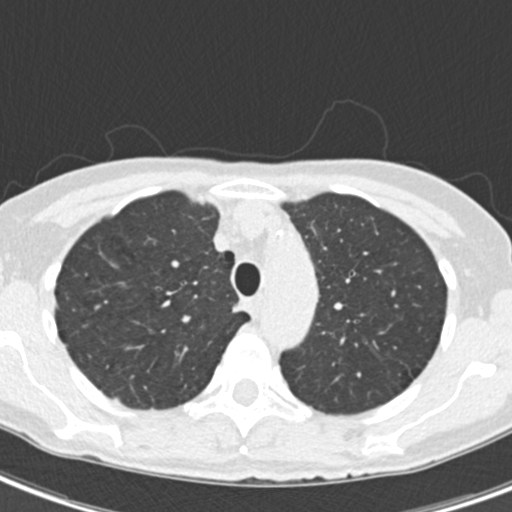
Axial slice from a low-dose chest CT screening exam. Second screening round (one year after baseline). Lung window (W 1500 / L -600 HU). 2 mm slice thickness. Slice 48 of 218 in the series. Female, age 68 years at enrolment. Current smoker at enrolment.
- Expert-annotated lung lesion, bounding box <224,300,253,326> (left, top, right, bottom; pixels).
- No non-calcified nodule or mass ≥4 mm was recorded by the screening reader at this exam.
- Official screen result: negative screen, no significant abnormalities.
- Later outcome: lung cancer diagnosed 436 days after this screen — squamous cell carcinoma, NOS, right upper lobe, mediastinum, poorly differentiated (G3), stage IIIB (AJCC 6th edition), 43 mm at pathology.